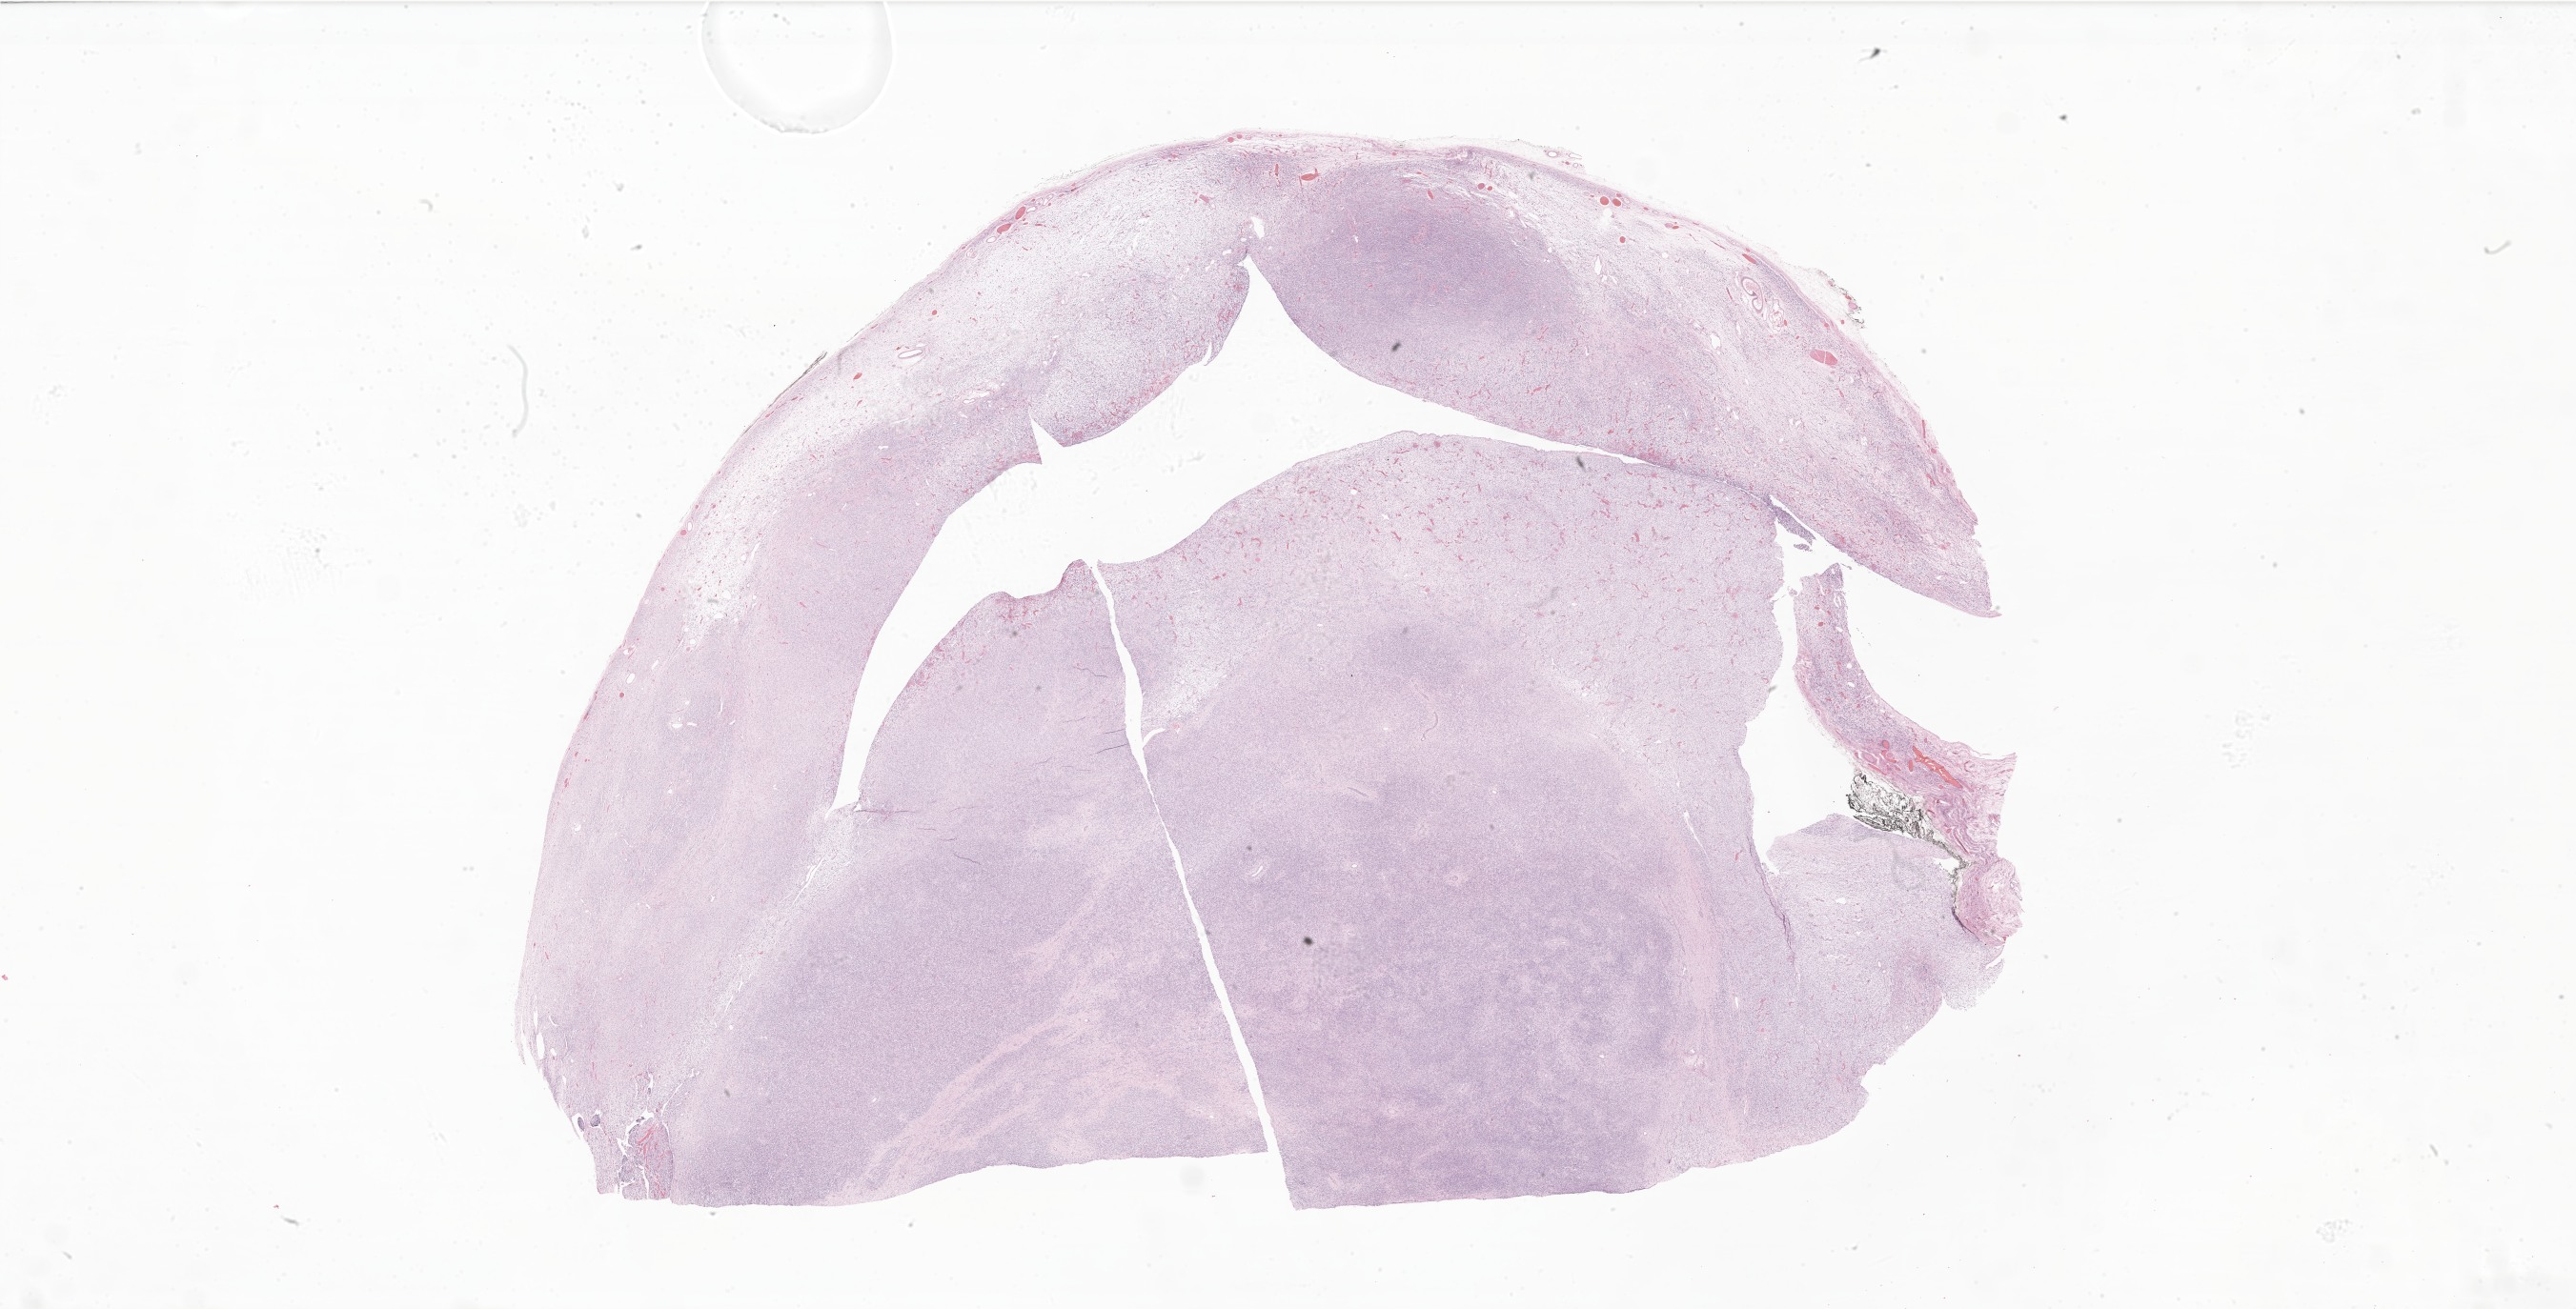
Whole-slide image, H&E stain of tumor tissue from the testis, a low-resolution overview of the entire scanned area, about 45.6 x 23.2 mm; formalin-fixed paraffin-embedded section. Patient: male, age 59 months.
• diagnosis: Rhabdomyoma, NOS